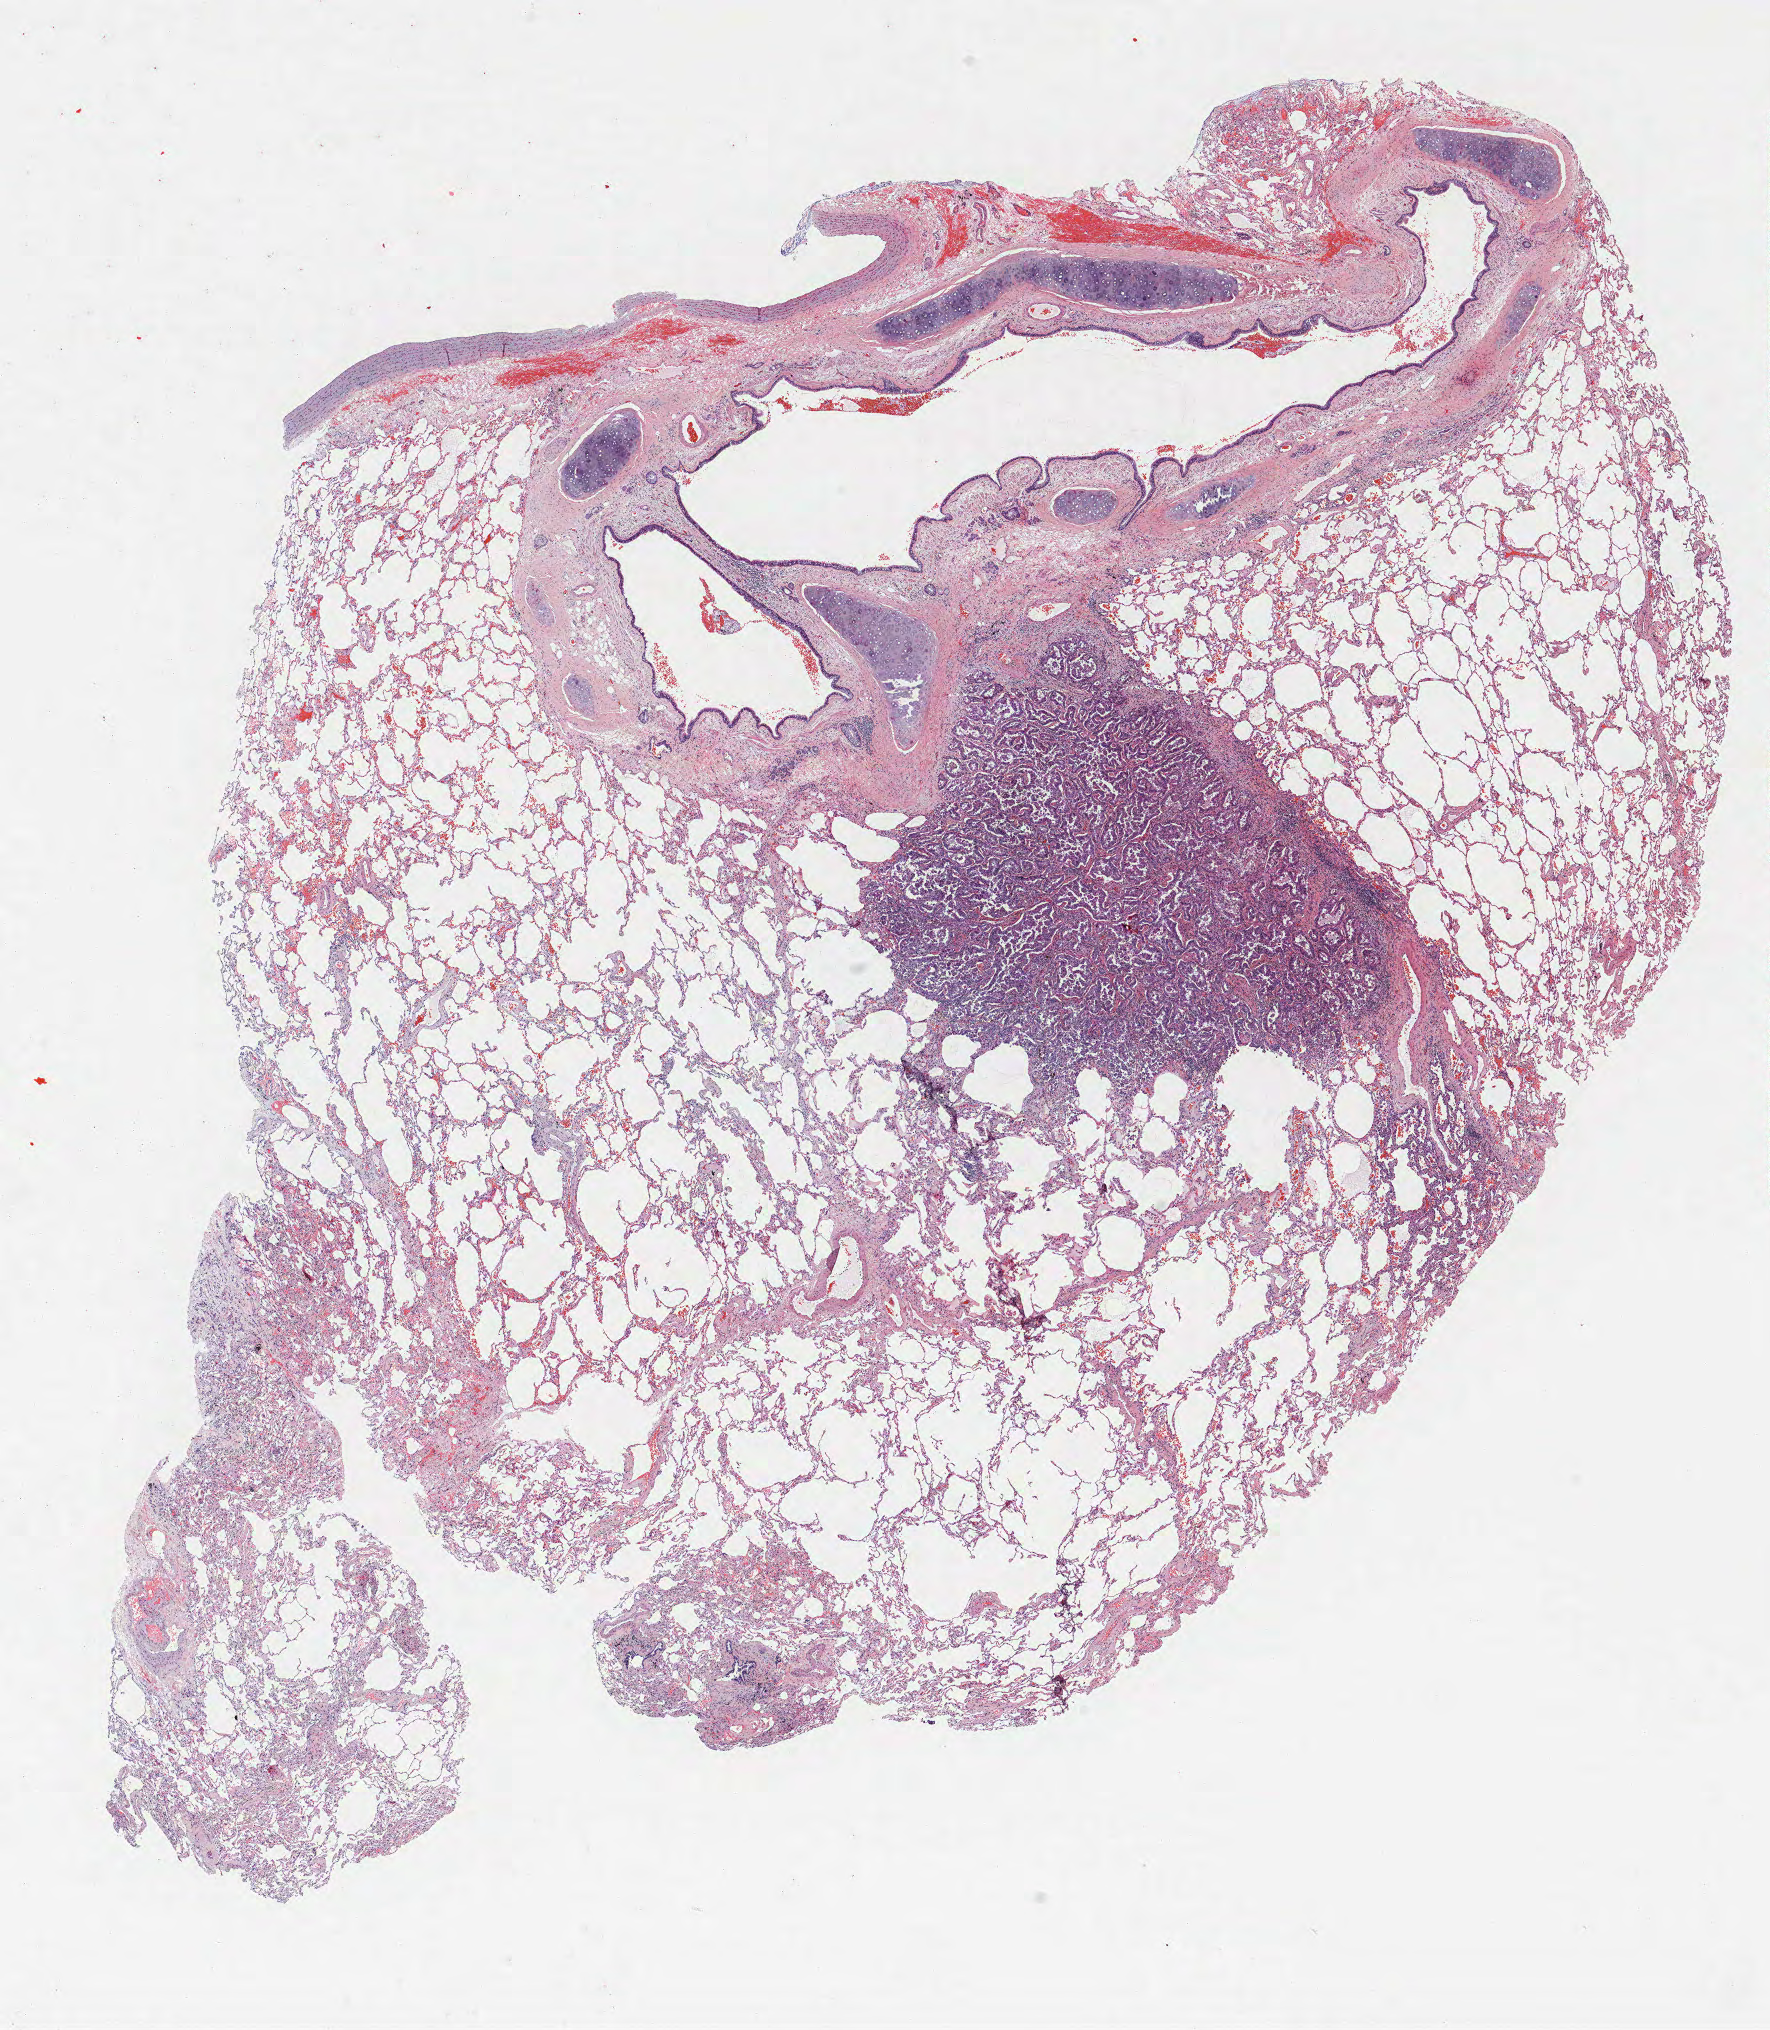
Whole-slide histology image, H&E-stained — a low-resolution overview of the entire scanned area, about 14.2 x 16.2 mm (slide scanned at 40x), formalin-fixed paraffin-embedded (FFPE) section, lung. Female, age 56 at enrolment. Grade: moderately differentiated (G2).
- tumour size (pathology): 19 mm
- primary tumour location (clinical record): right upper lobe
- participant's lung-cancer diagnosis: Adenocarcinoma, NOS
- stage (AJCC 6th edition): IA